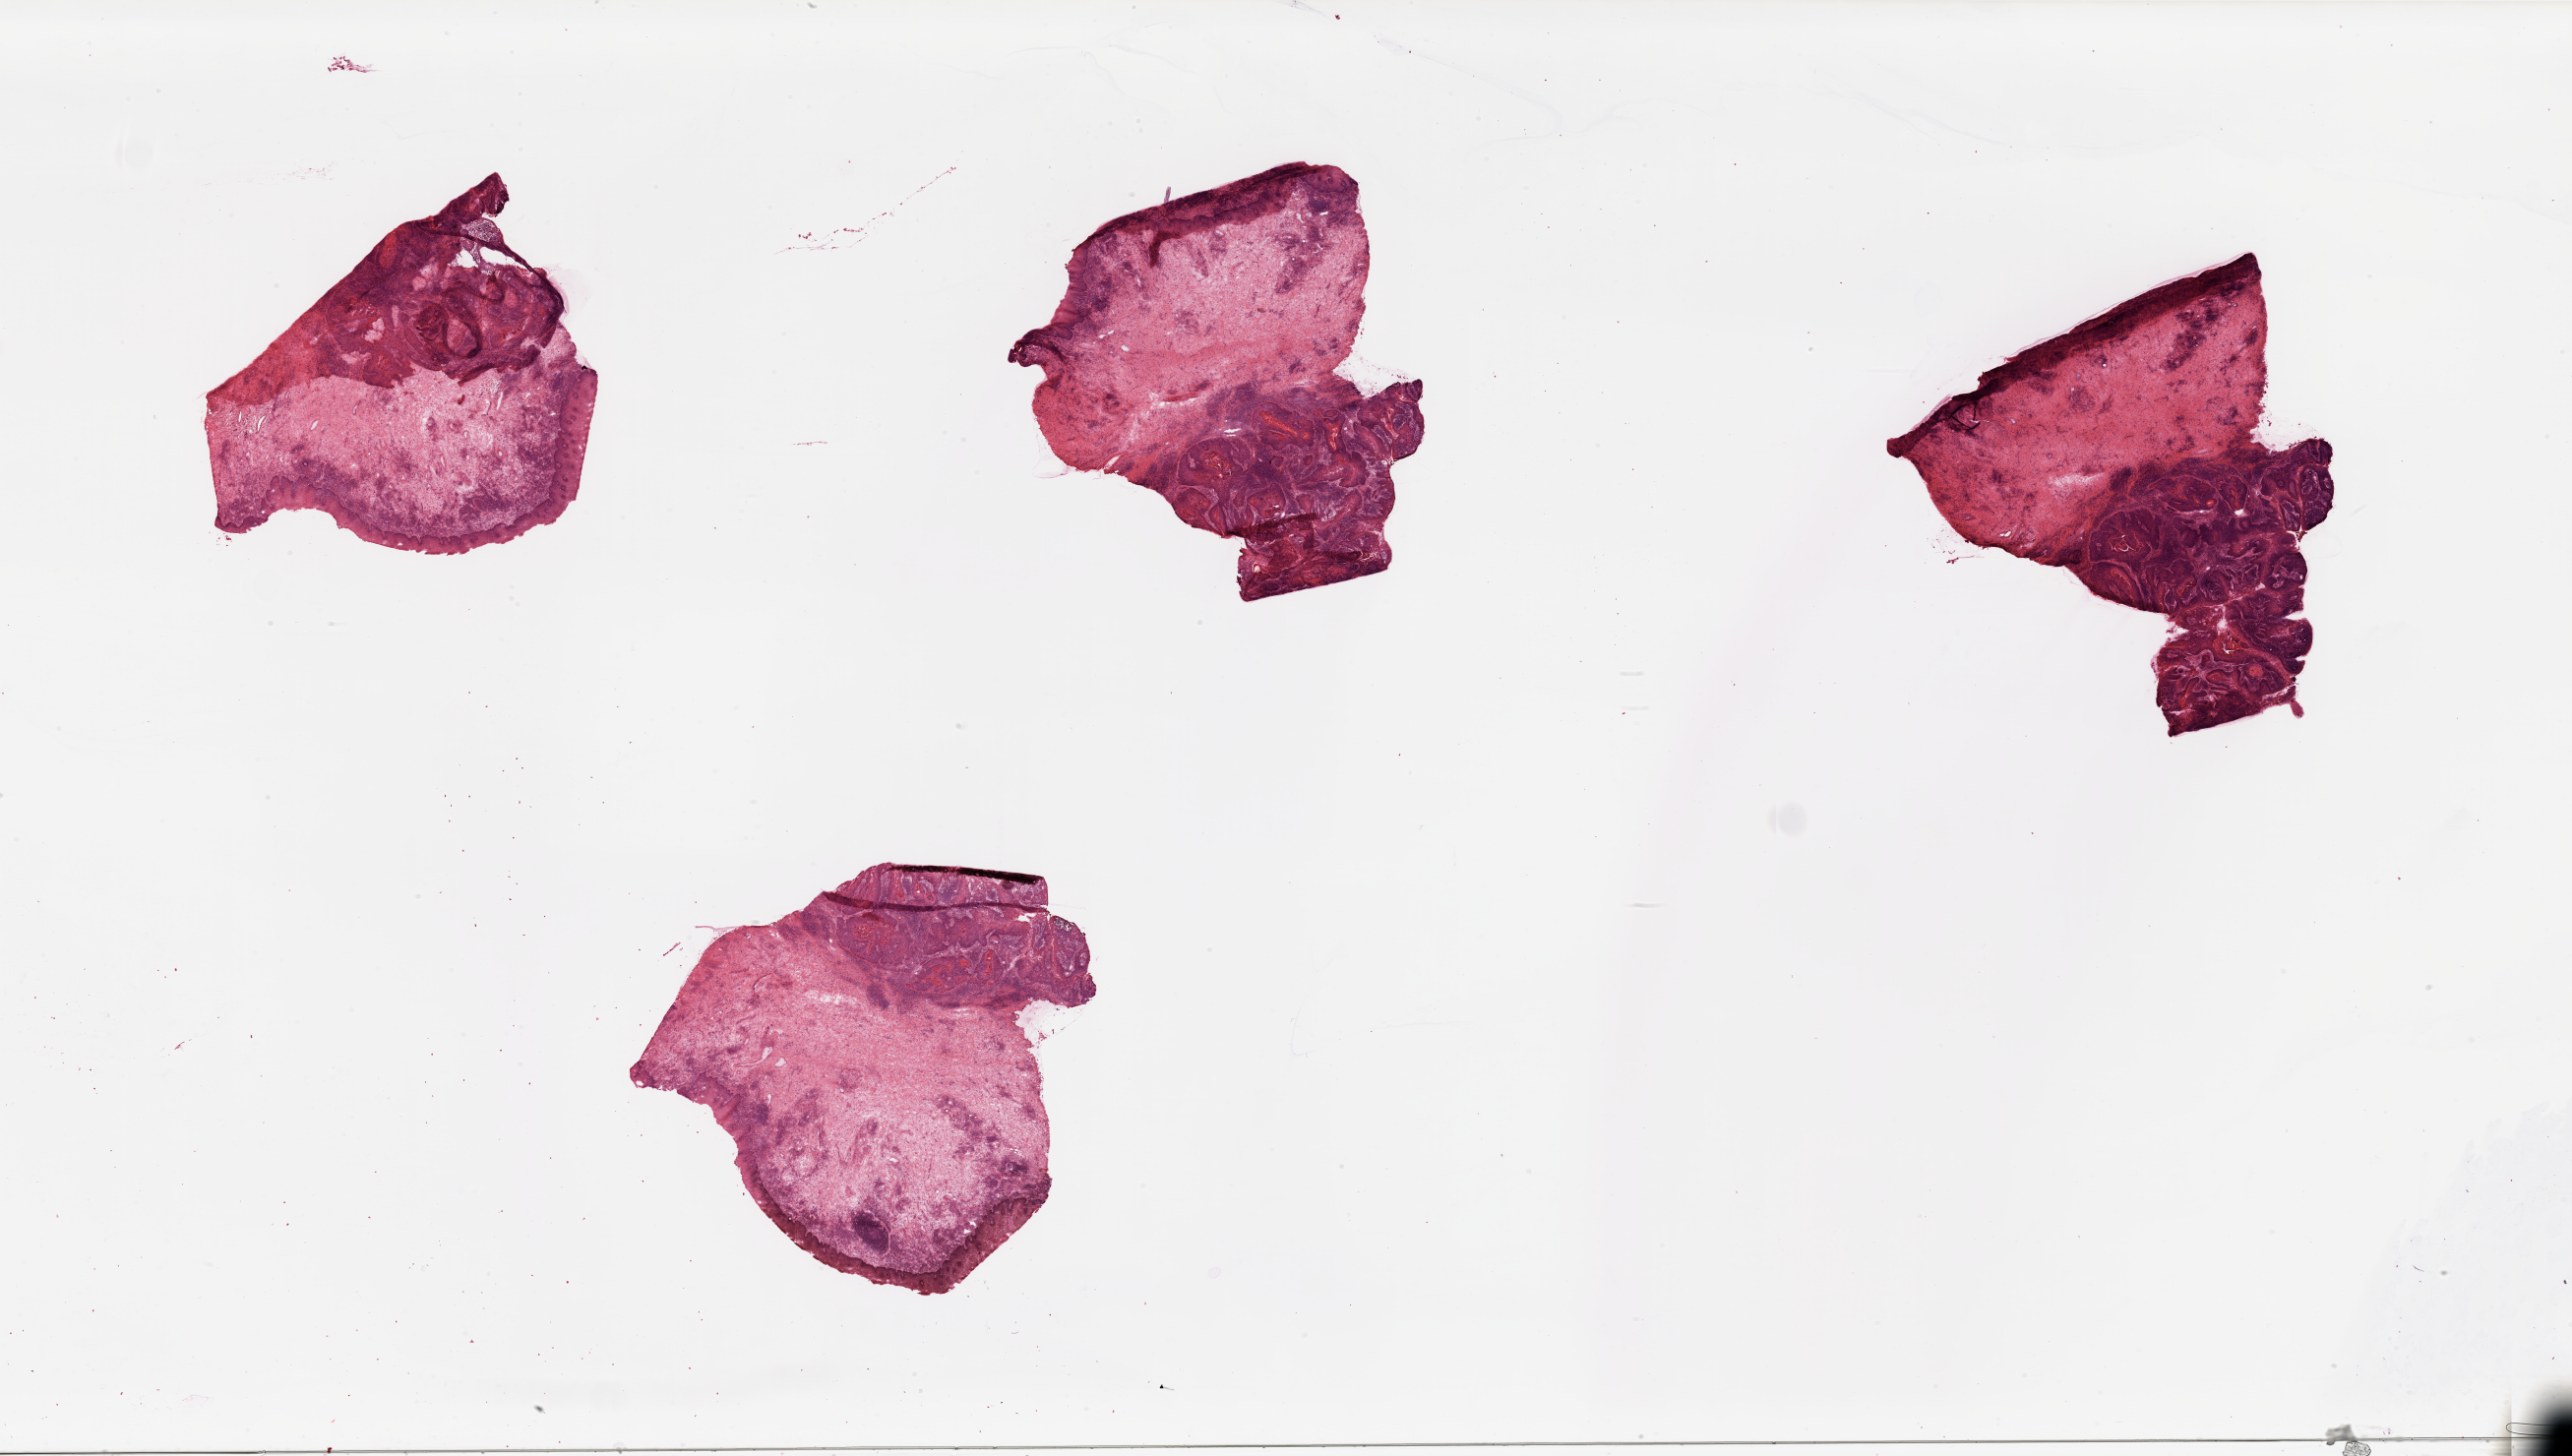
Hematoxylin and eosin (H&E) stained whole-slide image, whole scanned area (about 41.3 x 23.4 mm) shown as a low-resolution overview, head and neck, tissue type not recorded. Patient: male, age 67 years.
Patient diagnosis: Squamous cell carcinoma, NOS (larynx, NOS).